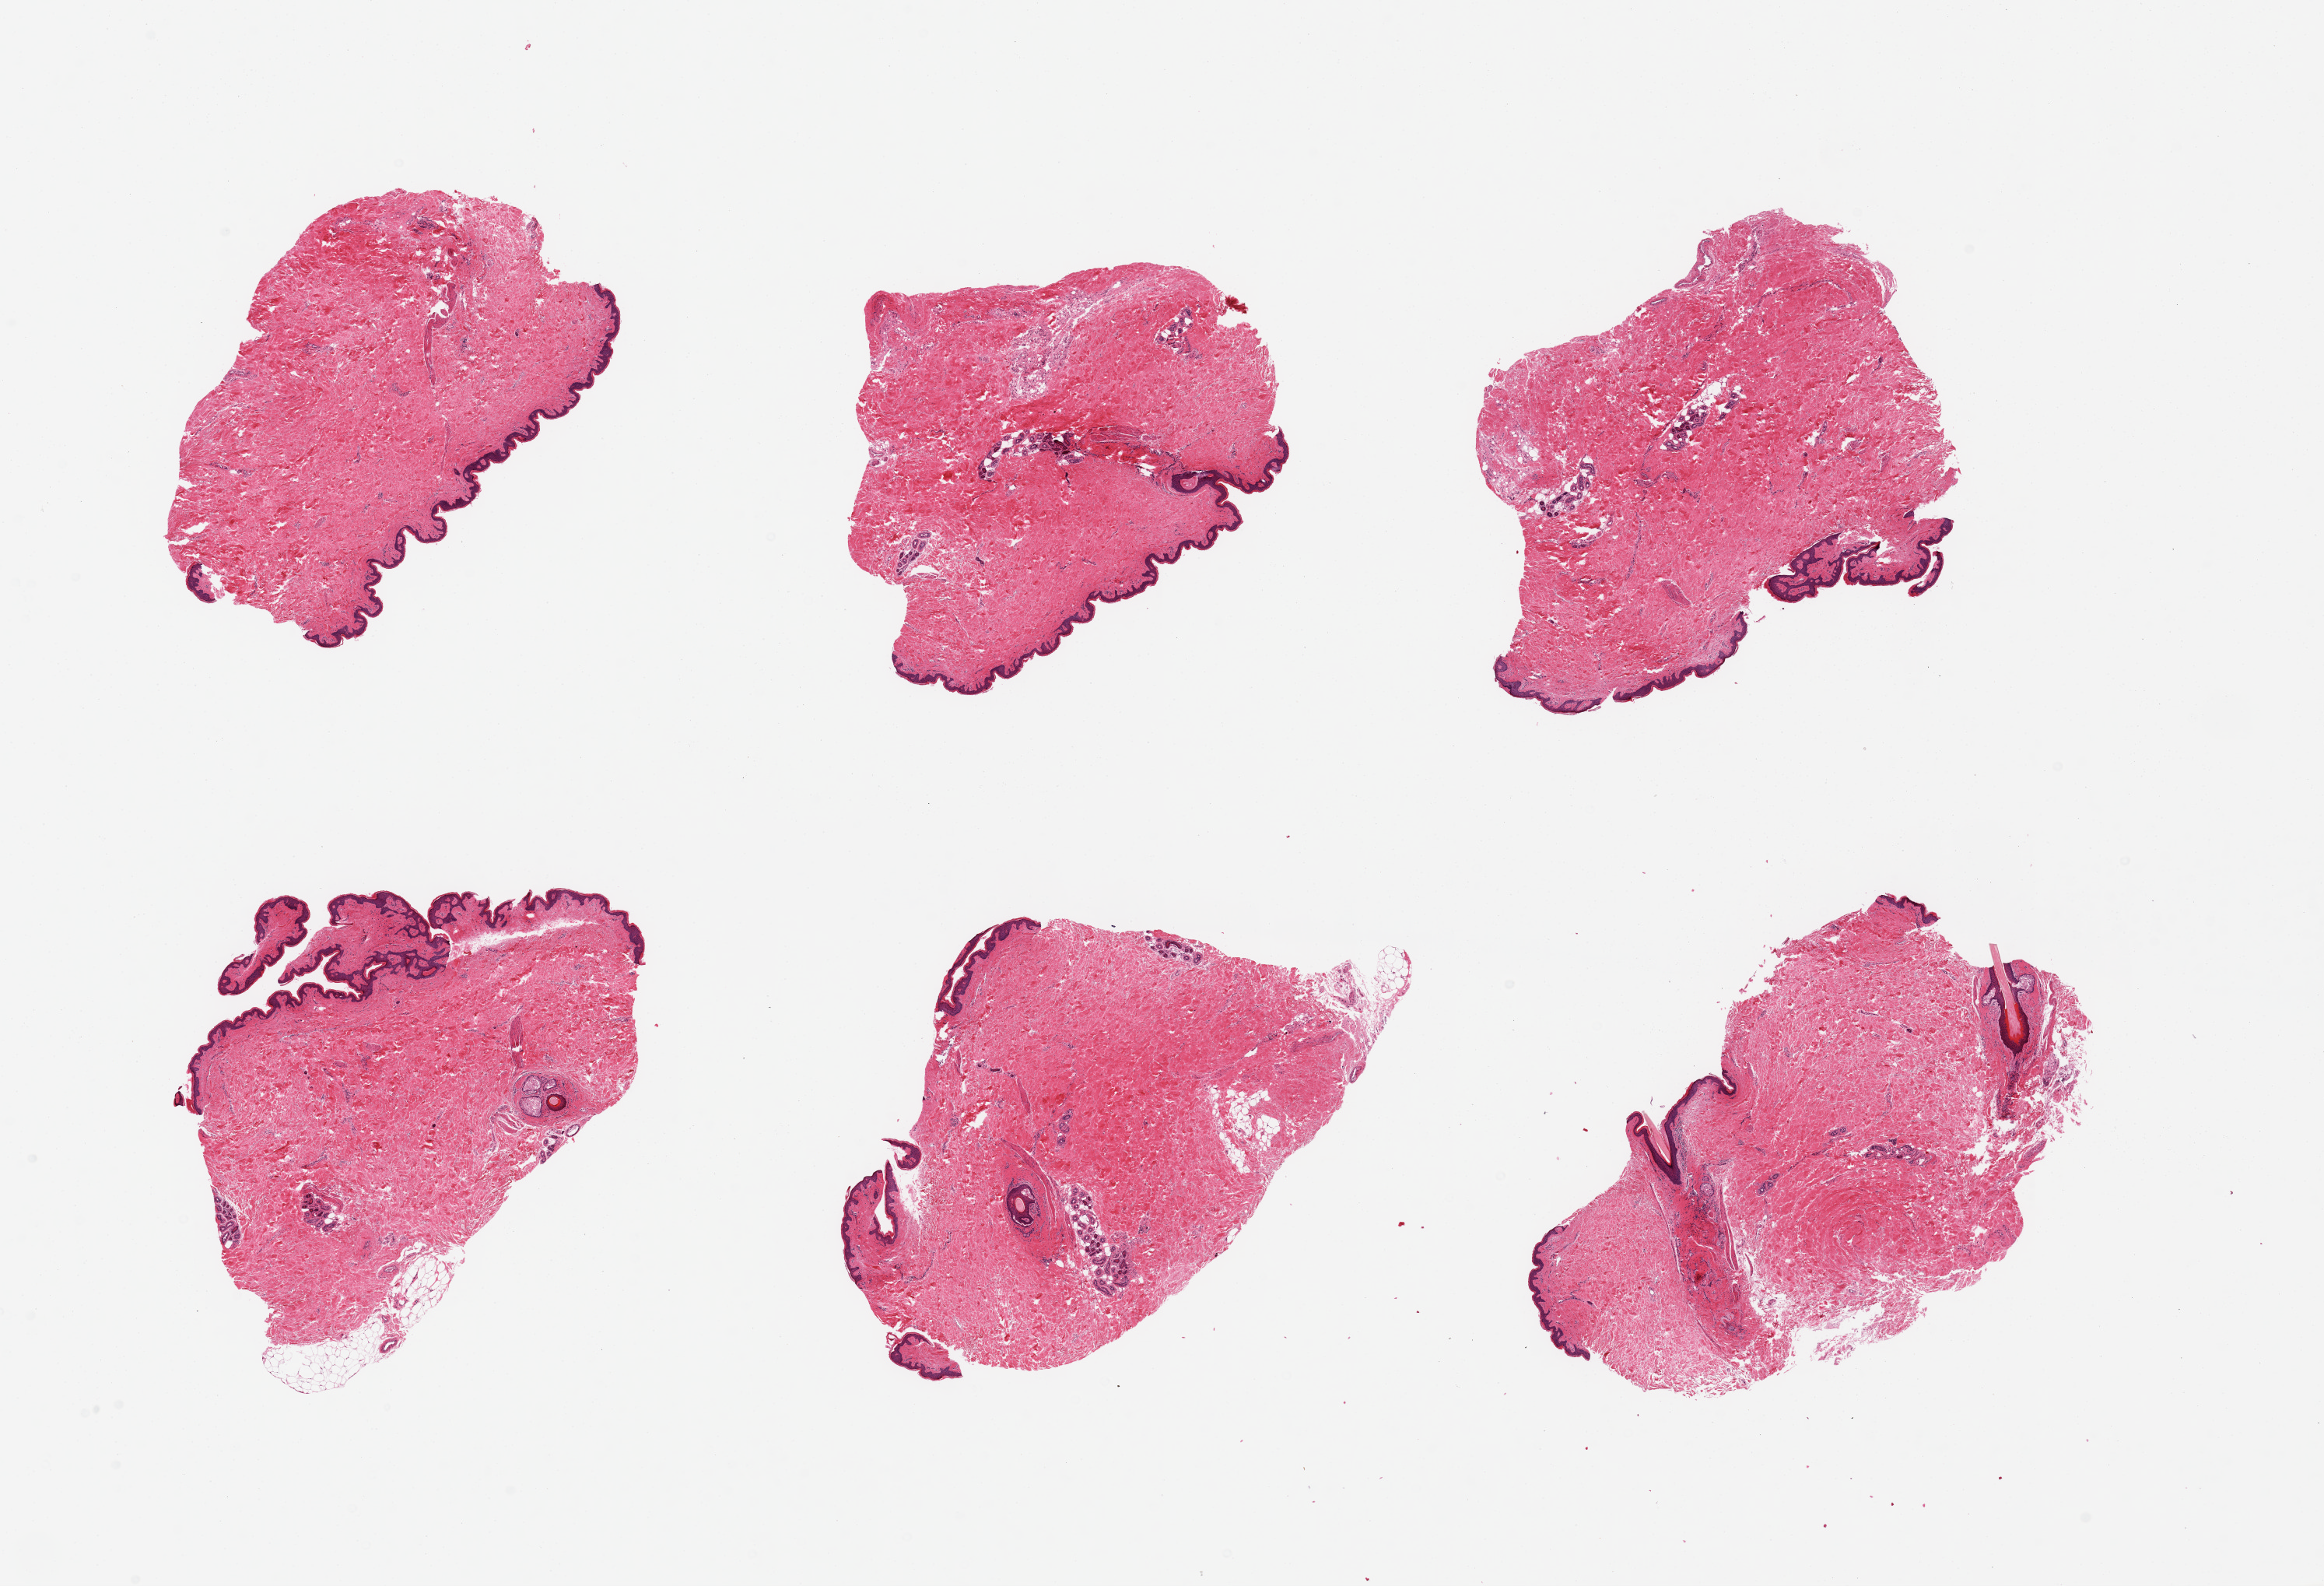
H&E whole-slide image, brightfield — a low-resolution overview of the entire scanned area, about 23.6 x 16.1 mm, PAXgene-fixed paraffin-embedded (PFPE) section, section of skin of suprapubic region (target tissue), donor tissue sample. Donor: male.
• pathologist's review note for this sample: 6 pieces, trace dermal fat, squamous epithelium is 30-45 microns